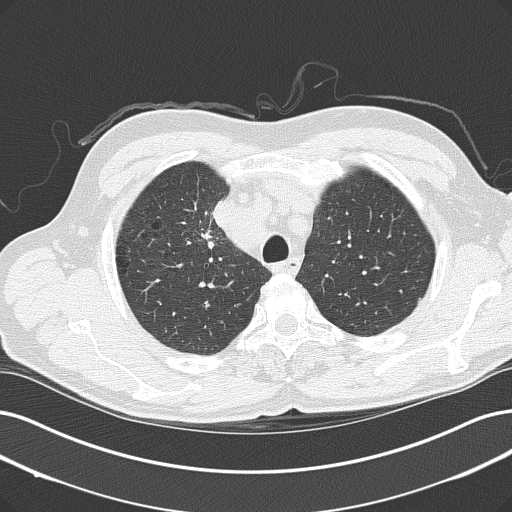
Axial slice from a low-dose chest CT screening exam, first (baseline) screen, lung window (W 1500 / L -600 HU), 2 mm slice thickness, 120 kVp, slice 35 of 152 in the series, 512 × 512 image matrix. Male, age 61 years at enrolment.
- Lesion marked by an expert reader, bounding box (x1, y1, x2, y2) in pixels: (188, 217, 246, 265).
- The screening reader recorded 2 non-calcified nodules or masses ≥4 mm on this exam; which of them this box marks is not recorded.
- Official screen result: positive, change unspecified: nodule(s) >= 4 mm or enlarging nodule(s), mass(es), or other non-specific abnormalities suspicious for lung cancer.